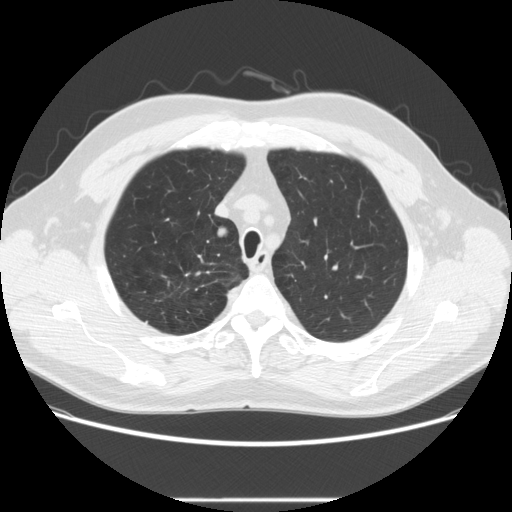
Axial slice from a low-dose chest CT screening exam; first (baseline) screen; lung window (W 1500 / L -600 HU); 2.5 mm slice thickness; slice 49 of 270 in the series. Male participant, aged 64 years at enrolment.
Expert-annotated lung lesion, box from (x=194, y=220) to (x=239, y=254) px. The screening reader recorded 2 non-calcified nodules or masses ≥4 mm on this exam (right upper lobe, right upper lobe); which of them this box marks is not recorded. Official screen result: positive, change unspecified: nodule(s) >= 4 mm or enlarging nodule(s), mass(es), or other non-specific abnormalities suspicious for lung cancer. Participant outcome: lung cancer diagnosed 753 days after this screen — adenocarcinoma, NOS, right upper lobe, moderately differentiated (G2), stage IA (AJCC 6th edition), 14 mm at pathology.